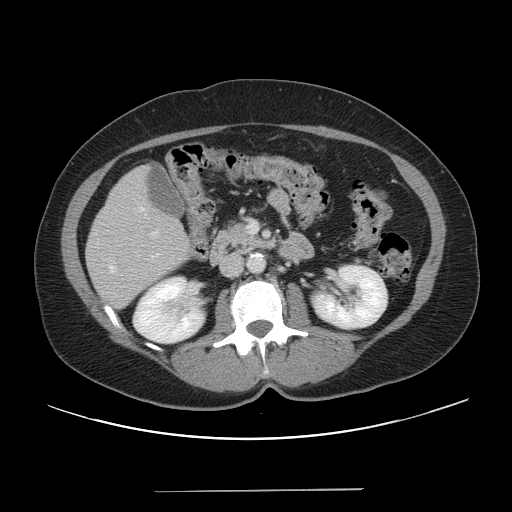
Contrast-enhanced abdominal CT, one axial slice; slice 18 of 56 in the series (ordered by position); intravenous contrast given; soft-tissue window (W 400 / L 40 HU); 5 mm slice thickness; 512 × 512 image matrix. Female patient, age 54 years. From the clinical record (not read from this slice): diagnosis: colorectal cancer liver metastases, imaged before liver resection; multiple liver metastases: yes; largest metastasis: 3.2 cm; disease in both lobes: yes.
Annotated regions visible in this slice (expert manual segmentation):
- hepatic veins: box from (x=110, y=266) to (x=114, y=272) px
- liver: (x=87, y=167)–(x=191, y=311)
- portal vein (with intrahepatic branches): (x=152, y=223)–(x=257, y=235)